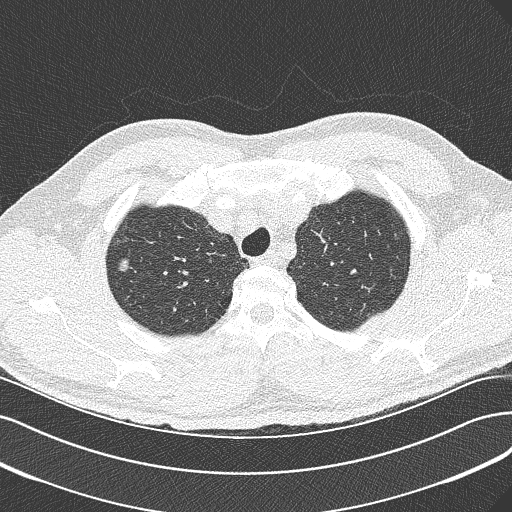
Chest CT (low-dose screening protocol), one axial image, first (baseline) screen, lung window (W 1500 / L -600 HU), lung (sharp) reconstruction kernel (B50f). Male, age 56 years at enrolment. Current smoker at enrolment.
Expert reader's lesion annotation, bounding box [x1, y1, x2, y2] px = [102, 248, 139, 283]. Reader record for this screening exam (exam-level; its link to the box is not recorded): non-calcified nodule or mass ≥4 mm, right upper lobe, 10 × 7 mm, spiculated (stellate) margins, soft tissue attenuation. Lung cancer was diagnosed 517 days after this screen (after the second annual screen): bronchiolo-alveolar carcinoma, non-mucinous, right upper lobe, moderately differentiated (G2), stage IIIB (AJCC 6th edition), 10 mm at pathology.